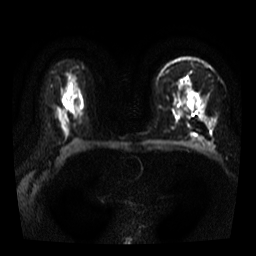
Breast MRI, one axial slice; diffusion-weighted series; image 2 of 4 stored at this slice position (different b-values; order by instance number); 3 T; 5 mm slice thickness; 256 × 256 image matrix. Female patient.
Outlined on this slice (manually delineated by an expert):
- tumour on diffusion-weighted imaging: box from (x=202, y=98) to (x=206, y=101) px